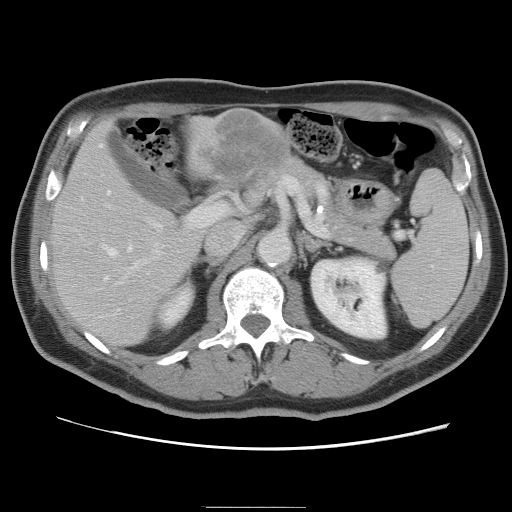
Contrast-enhanced abdominal CT, one axial slice; slice 46 of 87 in the series (ordered by position); 120 kVp; intravenous contrast given; soft-tissue window (W 400 / L 40 HU); 512 × 512 image matrix, field of view 363 × 363 mm. Male patient, age 63 years. Case-level facts recorded for this patient, not image findings: diagnosis: colorectal cancer liver metastases, imaged before liver resection; multiple liver metastases: no; largest metastasis: 9 cm; disease in both lobes: no.
Annotated regions visible in this slice (manually delineated by an expert):
- hepatic veins: bounding box <100,145,132,279> (left, top, right, bottom; pixels)
- liver: <51,108,293,346>
- planned liver remnant (the part of the liver to remain after resection): <50,146,200,346>
- portal vein (with intrahepatic branches): <106,205,204,285>
- liver metastasis: <204,113,283,189>